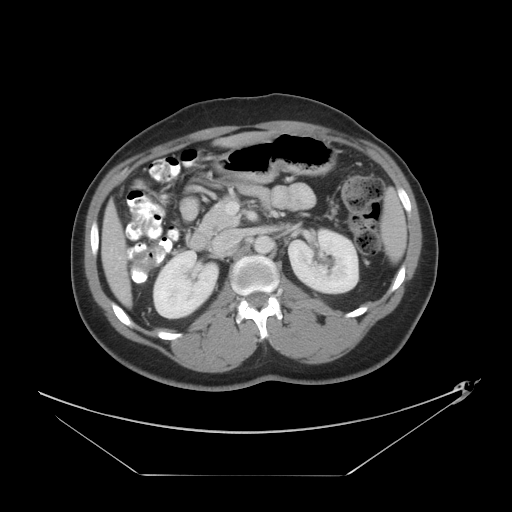
Contrast-enhanced abdominal CT, one axial slice. Position 19 of 44 along the scan axis. Reconstruction kernel STANDARD. 120 kVp. Intravenous contrast given. Soft-tissue window (W 400 / L 40 HU). 5 mm slice thickness. 512 × 512 image matrix, field of view 466 × 466 mm. Male patient, age 49 years. Case-level facts recorded for this patient, not image findings: diagnosis: colorectal cancer liver metastases, imaged before liver resection; multiple liver metastases: no; largest metastasis: 8.5 cm; disease in both lobes: yes.
Structures marked on this image (manually delineated by an expert):
- hepatic veins: bounding box <119,230,134,280> (left, top, right, bottom; pixels)
- liver: <102,132,271,307>
- planned liver remnant (the part of the liver to remain after resection): <217,132,271,148>